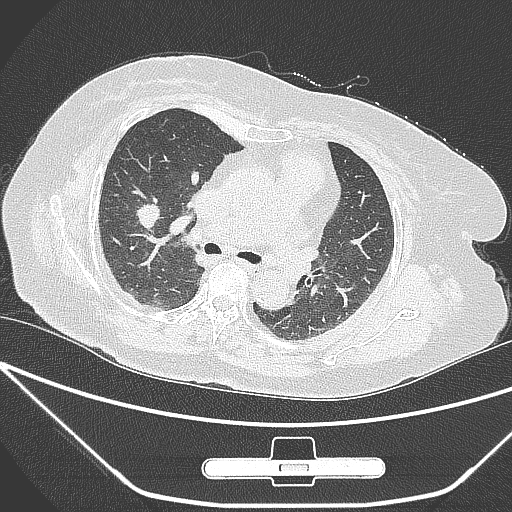
Chest CT, one axial slice. Position 162 of 245 along the scan axis. 120 kVp. Lung window (W 1500 / L -600 HU). 512 × 512 image matrix, field of view 365 × 365 mm. Patient: female, 65 years. From the clinical record (not read from this slice): clinical TNM (as recorded): T1c N0 M0; histopathological grade: G3.
Annotated regions visible in this slice (rectangle marked by the reading radiologist):
- lung tumour (recorded histology: adenocarcinoma): bounding box [x1, y1, x2, y2] px = [125, 195, 162, 236]